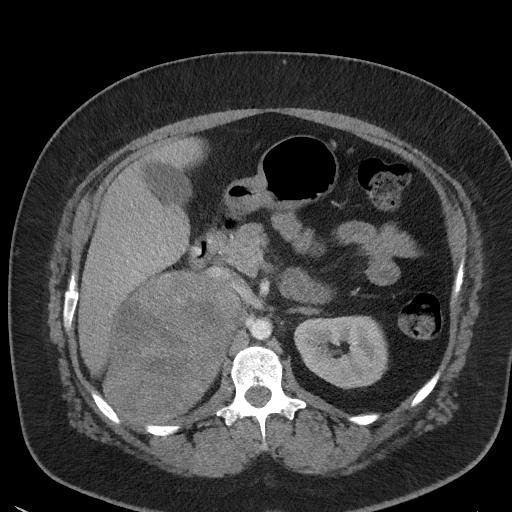
Contrast-enhanced abdominal CT, one axial slice; slice 28 of 56 in the series (ordered by position); intravenous contrast given; soft-tissue window (W 400 / L 40 HU); 5 mm slice thickness; 512 × 512 image matrix. Patient: female, 35 years. From the clinical record (not read from this slice): diagnosis: adrenocortical carcinoma; tumour side: right adrenal; tumour size at pathology: 15 cm; Ki-67 index: 40 %; stage (as recorded): 2.
Annotated regions visible in this slice (semi-automatically segmented with operator editing):
- mass: bounding box <108,274,238,422> (left, top, right, bottom; pixels)